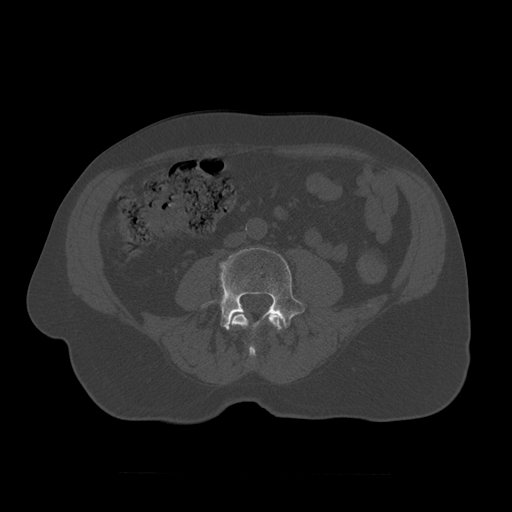
CT including the spine, one axial slice. Position 283 of 450 along the scan axis. Reconstruction kernel STANDARD. 120 kVp. Bone window (W 1800 / L 400 HU). 512 × 512 image matrix, field of view 405 × 405 mm. Patient age 75 years. Case-level facts recorded for this patient, not image findings: primary cancer: prostate.
Annotated regions visible in this slice (semi-automatically segmented with operator editing):
- L3 vertebra: bounding box <229,312,283,358> (left, top, right, bottom; pixels)
- L4 vertebra: <202,248,306,331>